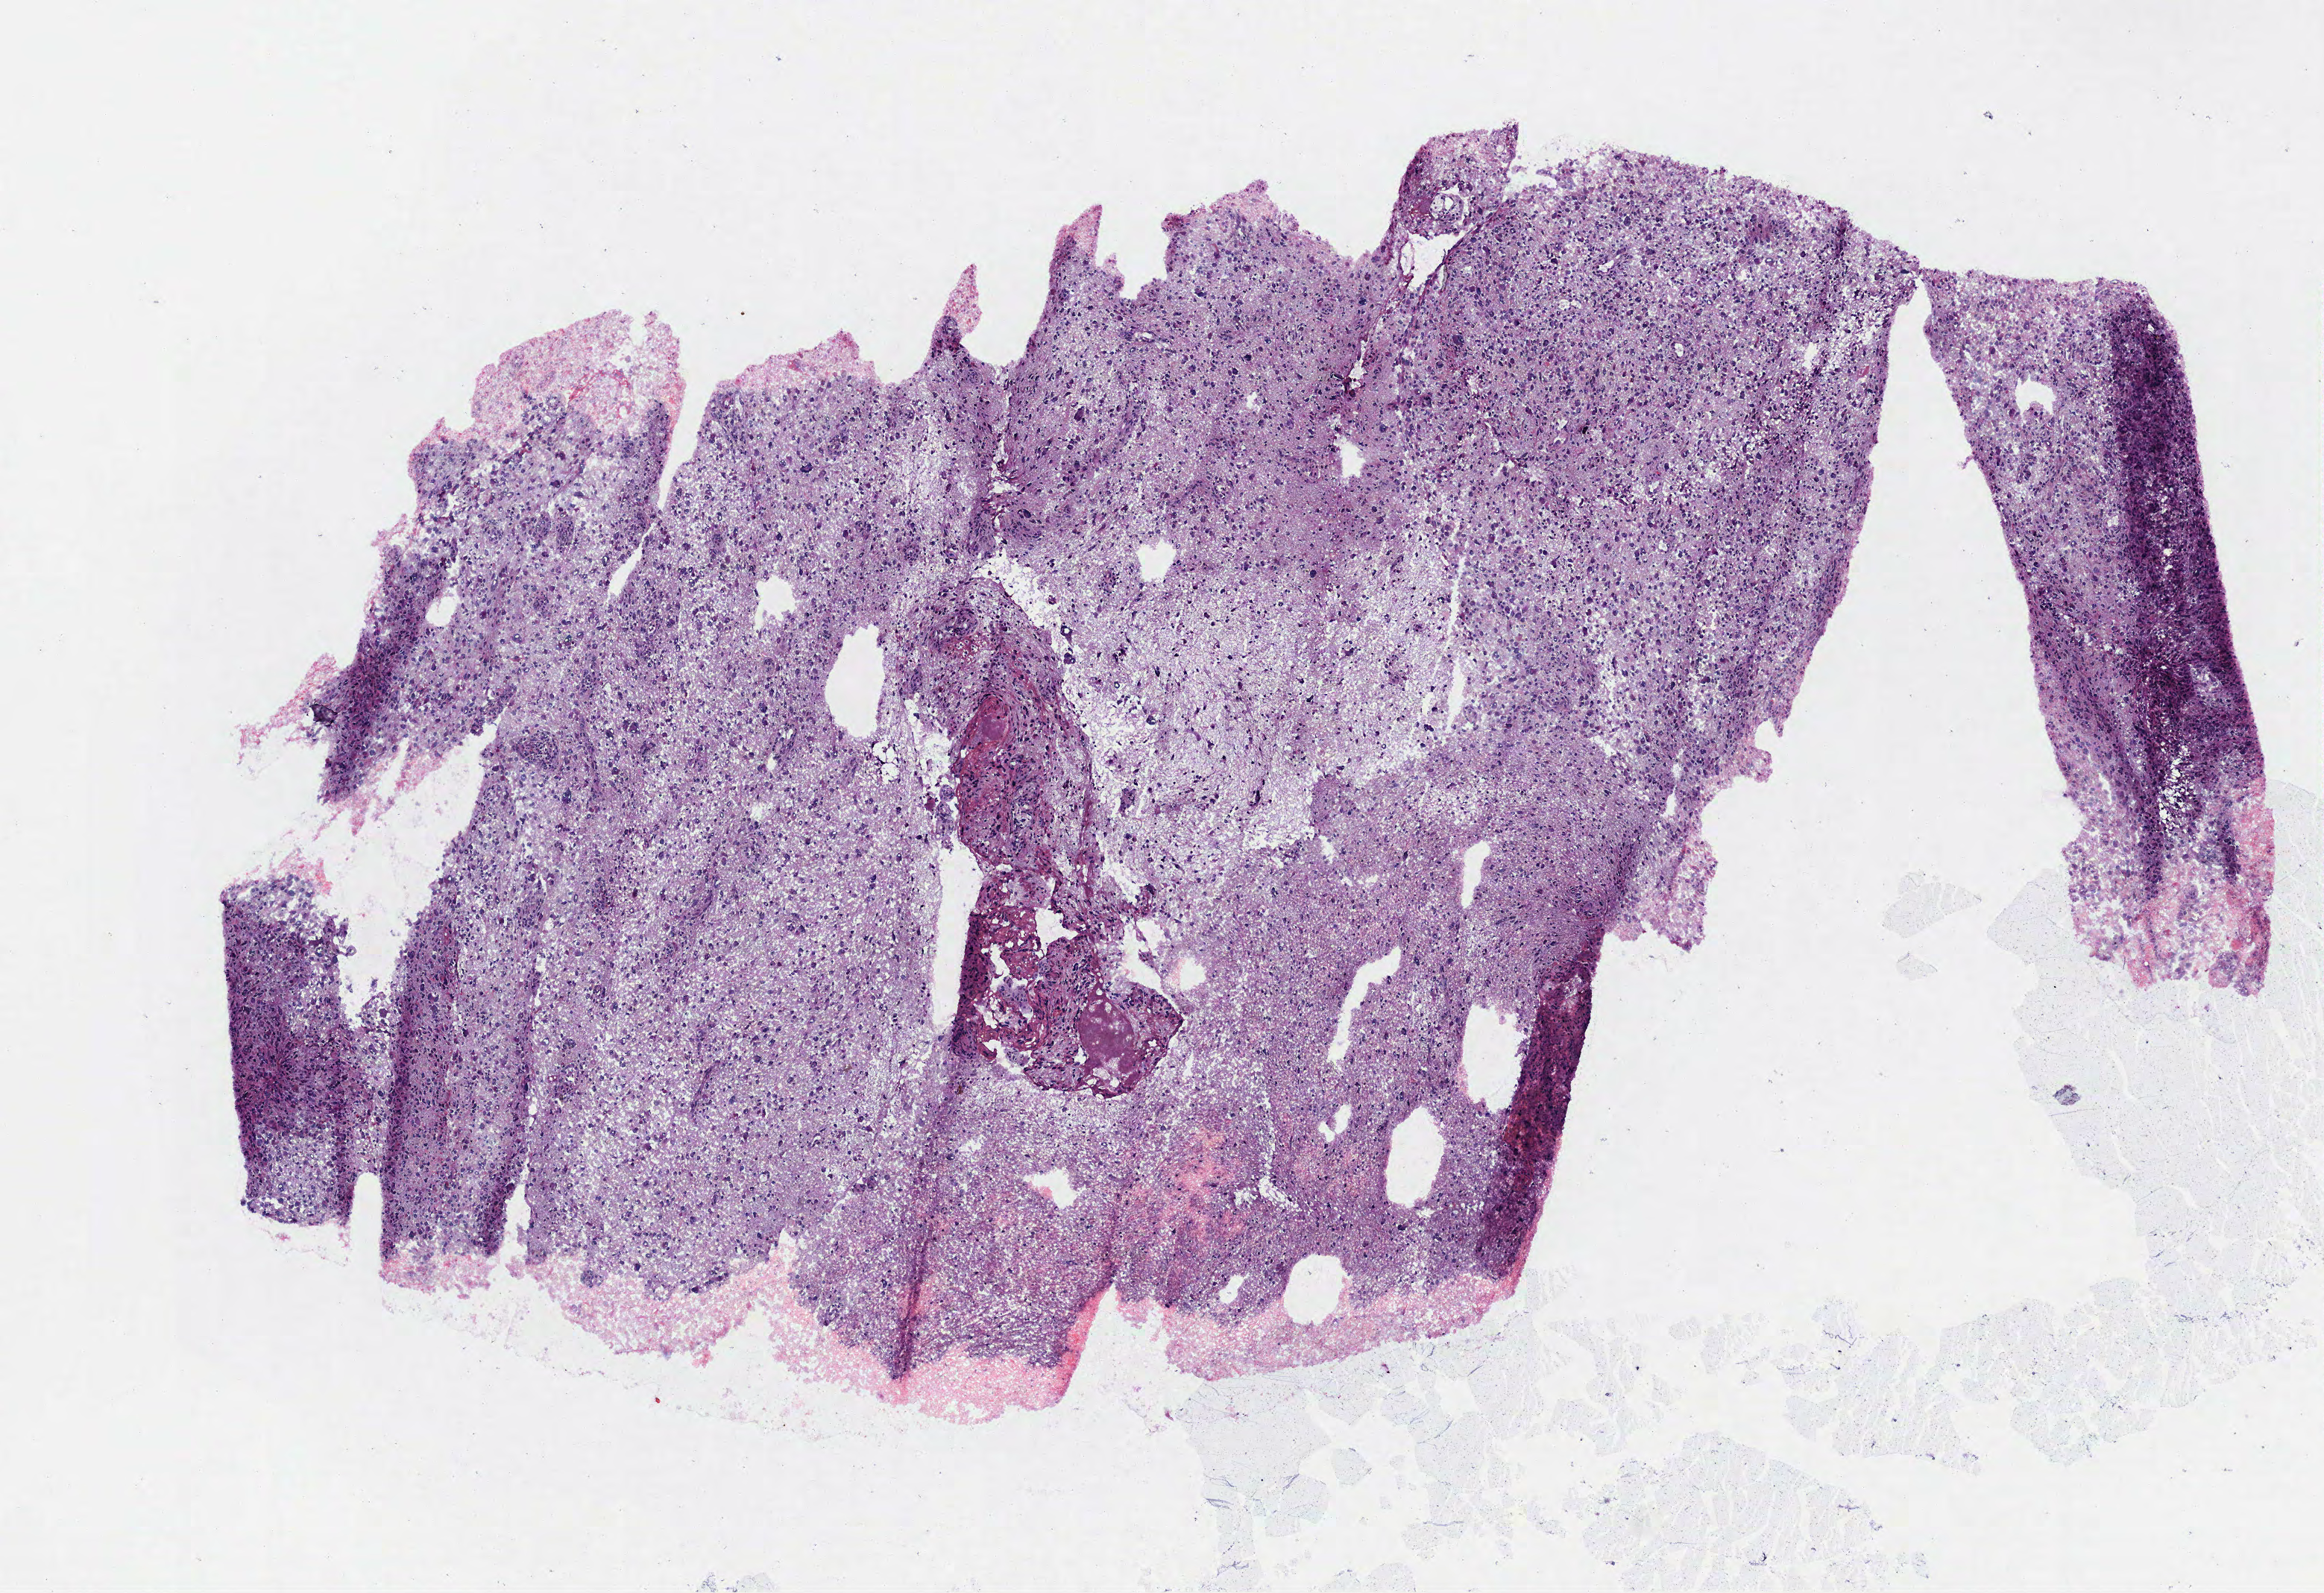
Hematoxylin and eosin (H&E) stained whole-slide image, low-resolution overview of the scanned area, about 6.3 x 4.3 mm (slide scanned at 40x). Frozen section from the top of the tissue portion. Brain, primary tumour sample. Female, age 24 years at initial diagnosis. Histologic grade: G3 (poorly differentiated). Pathologist review of this section (percent, as recorded): tumour cells 95%, tumour nuclei 70%, normal cells 0%, stromal cells 5%, necrosis 0%.
- histologic diagnosis: Astrocytoma, anaplastic (cerebrum)
- laterality: left